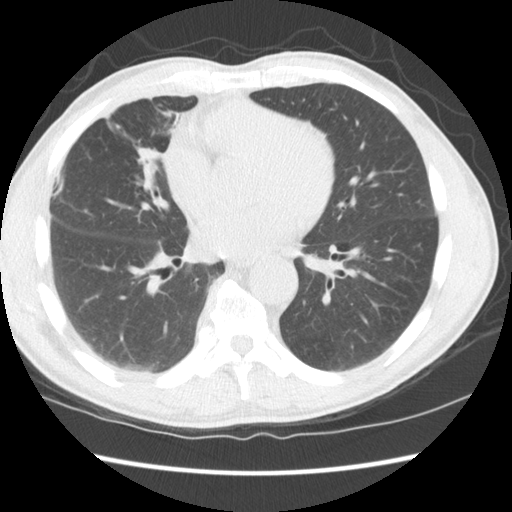
Low-dose screening chest CT, one axial slice; position 64 of 147 along the scan axis; 120 kVp; lung window (W 1500 / L -600 HU); 2.5 mm slice thickness; 512 × 512 image matrix, field of view 345 × 345 mm.
Structures marked on this image (manually delineated by an expert):
- lesion 1 (tumor, middle lobe of right lung): box from (x=141, y=148) to (x=162, y=170) px